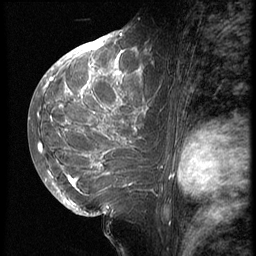
Breast MRI (dynamic contrast-enhanced), one sagittal slice. Position 32 of 62 along the scan axis. 3 images stored at this slice position (order not interpretable as contrast timing). 1.5 T. TE 4.2 ms, TR 9 ms. 256 × 256 image matrix. Patient: female, 28 years. Case-level facts recorded for this patient, not image findings: setting: breast cancer imaged before/during neoadjuvant chemotherapy.
Annotated regions visible in this slice (semi-automatic segmentation, software-assisted and operator-edited):
- analysis volume of interest (the breast-tissue region the enhancement analysis was run in; not a lesion): box from (x=42, y=45) to (x=162, y=207) px
- tumour enhancement mask (voxels above the 140 % enhancement threshold inside the analysis volume of interest): (x=45, y=45)–(x=153, y=191)